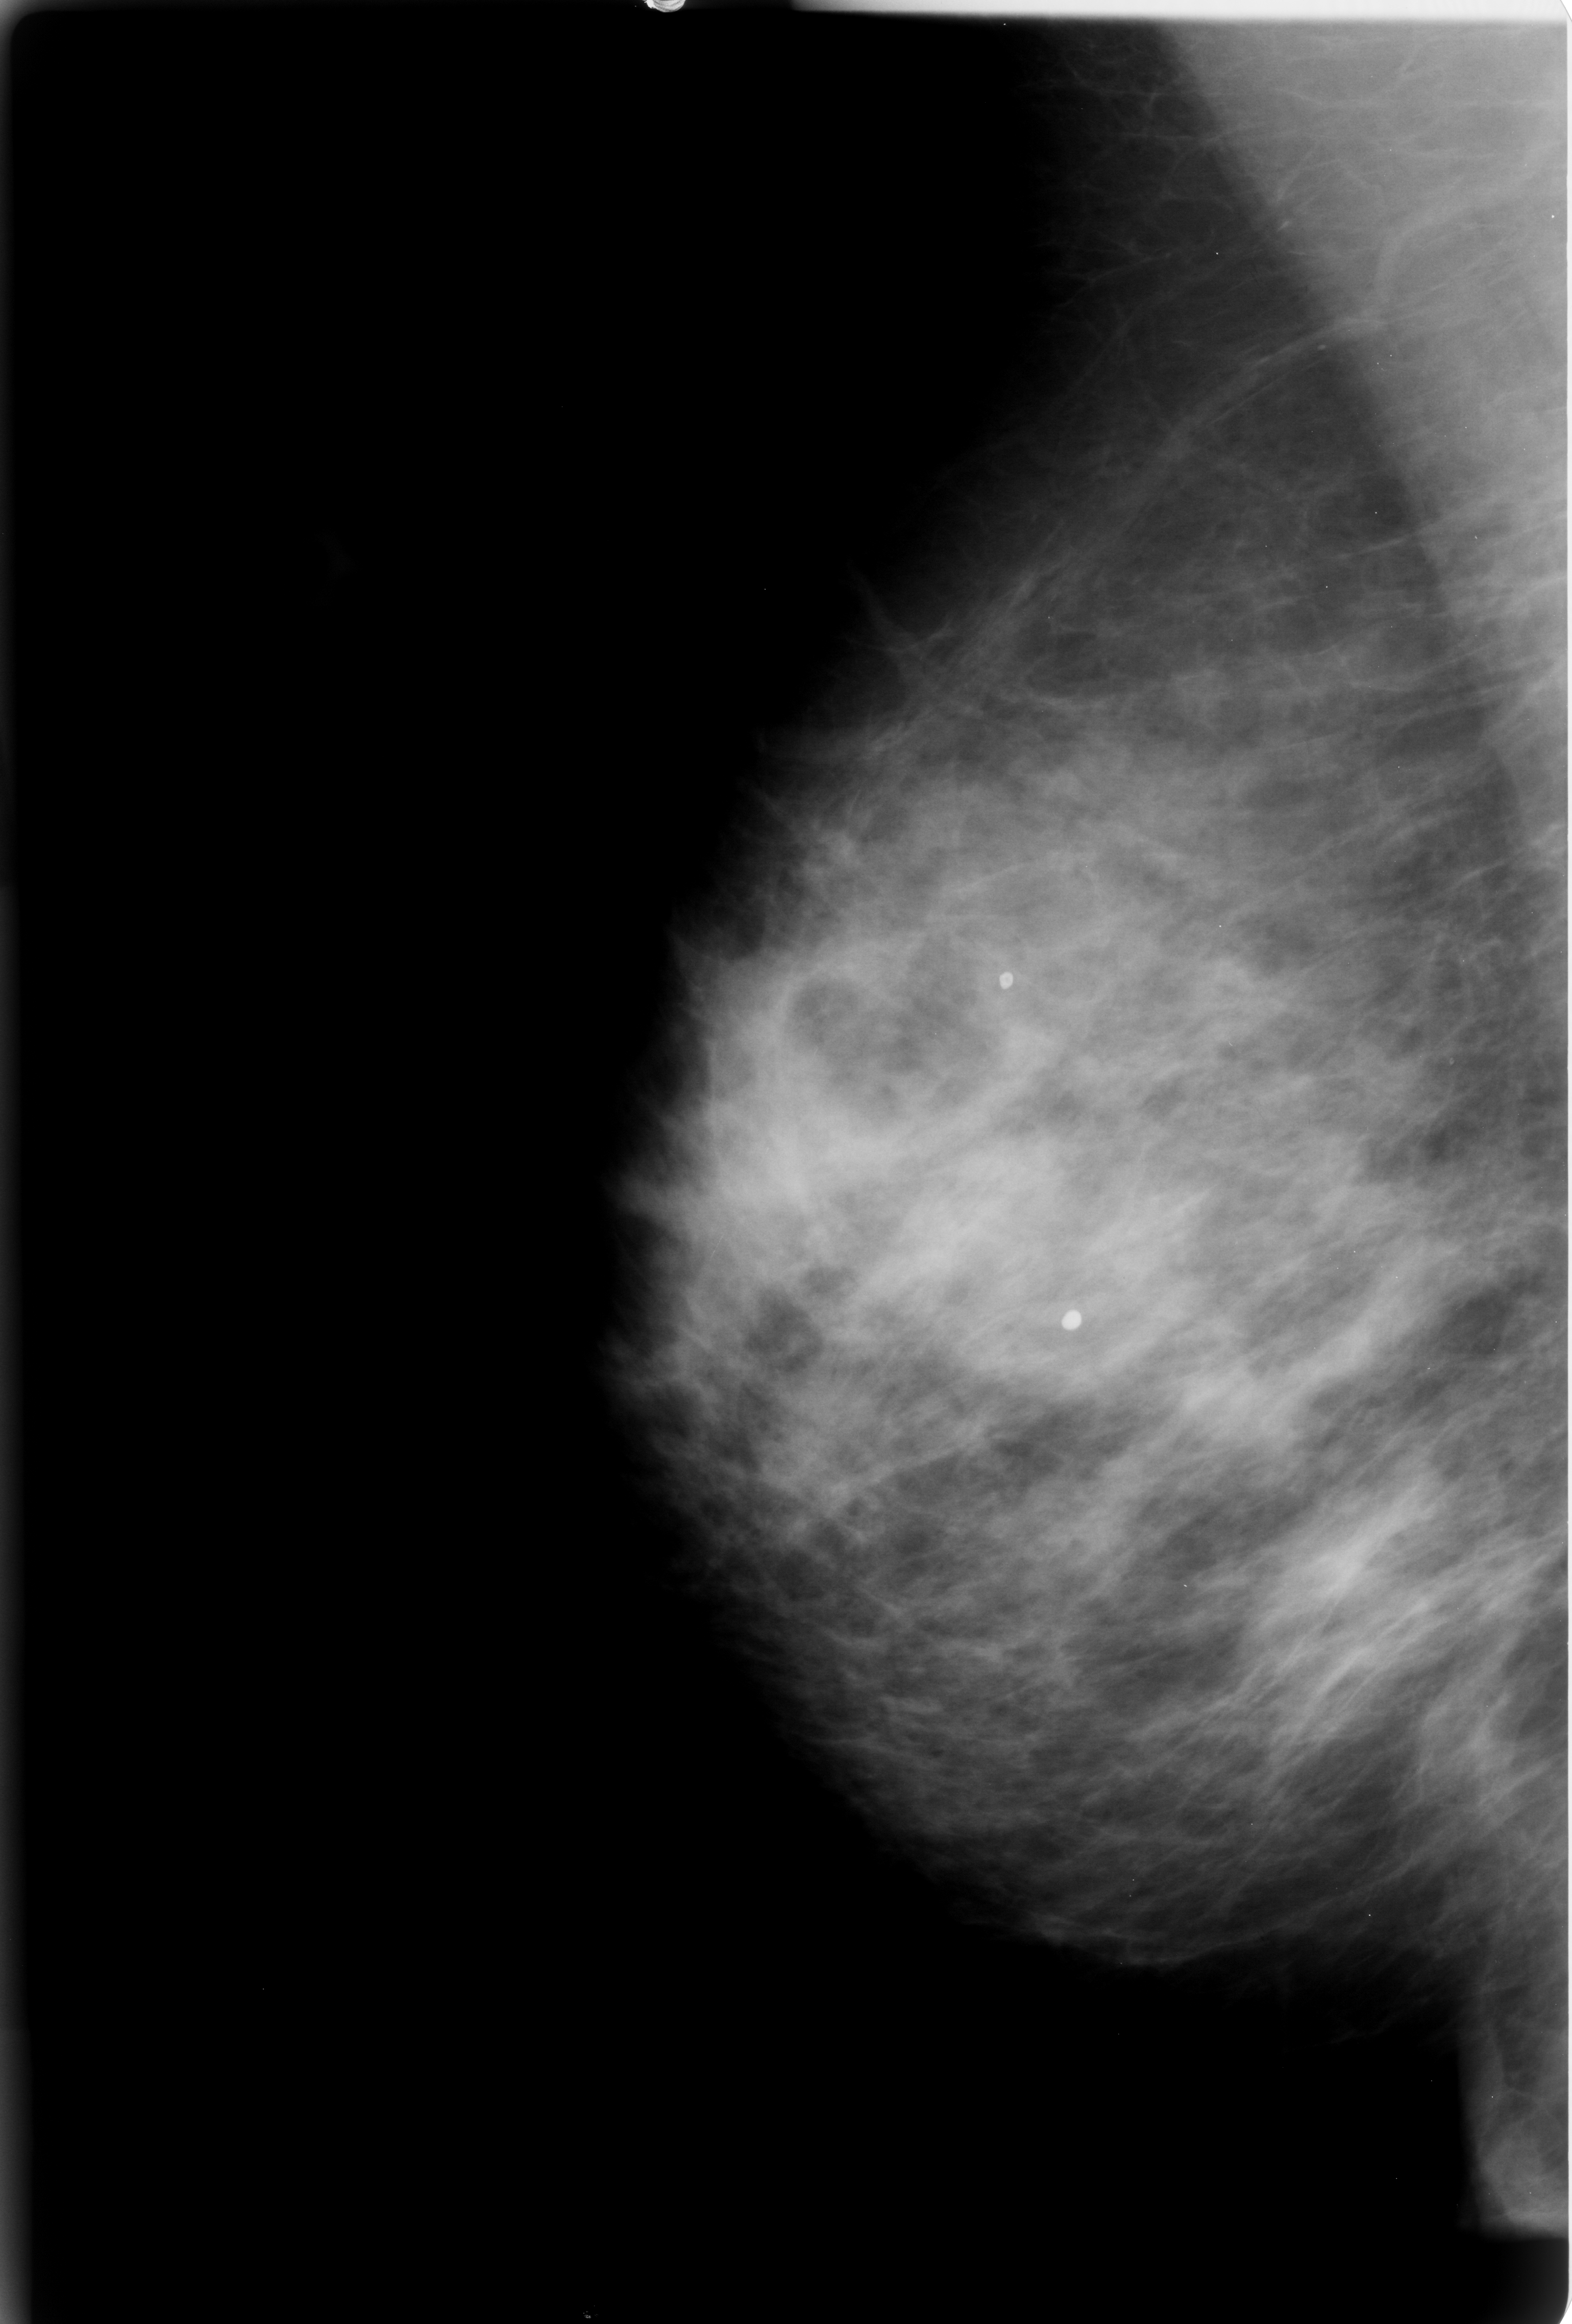
Scanned film-screen mammogram, right breast, MLO view, BI-RADS breast density category 3 (scale 1–4).
Abnormality record for this image: Finding 1 of 2: calcifications, morphology coarse / round and regular / lucent centered; BI-RADS assessment category 2; benign without callback (not worked up further). Finding 2 of 2: calcifications, morphology coarse / round and regular / lucent centered; BI-RADS assessment category 2; benign without callback (not worked up further).